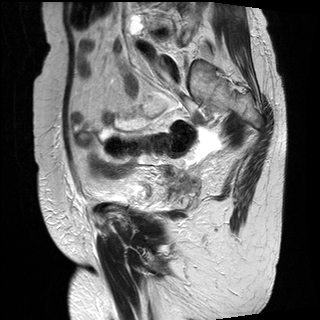
Pelvic MRI for cervical cancer, one sagittal slice. Slice 8 of 30 in the series (ordered by position). T2-weighted. 1.5 T. TE 89 ms, TR 2930 ms. 4 mm slice thickness. 320 × 320 image matrix. Female patient, age 61 years.
Annotated regions visible in this slice (expert manual segmentation):
- uterus and cervix: bounding box (x1, y1, x2, y2) in pixels: (161, 163, 202, 200)